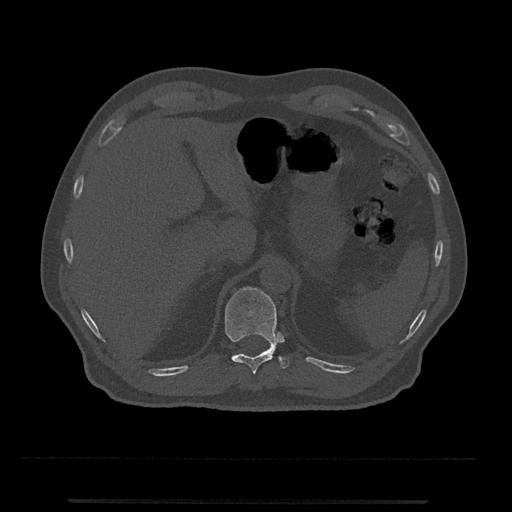
CT including the spine, one axial slice. Position 459 of 797 along the scan axis. Bone window (W 1800 / L 400 HU). 0.5 mm slice thickness. 512 × 512 image matrix. Patient: male, 63 years. From the clinical record (not read from this slice): primary cancer: prostate.
Structures marked on this image (semi-automatically segmented with operator editing):
- T11 vertebra: bounding box <225,287,289,374> (left, top, right, bottom; pixels)